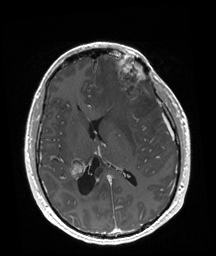
Brain MRI from a brain-tumour surgery series, one axial slice; slice 86 of 192 in the series (ordered by position); T1-weighted post-contrast; 1 mm slice thickness; 216 × 256 image matrix, field of view 219 × 260 mm. Case-level facts recorded for this patient, not image findings: tumour location: Left Frontal.
Outlined on this slice (outlined manually by an expert reader):
- tumour: box from (x=115, y=55) to (x=146, y=102) px